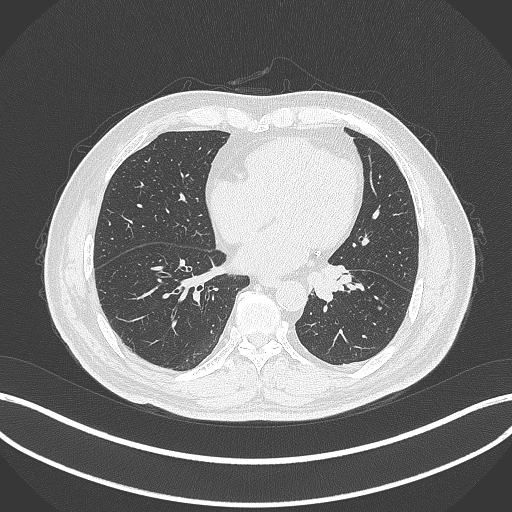
Chest CT, one axial slice; reconstruction kernel B70f; 120 kVp; lung window (W 1500 / L -600 HU); 1 mm slice thickness; 512 × 512 image matrix, field of view 400 × 400 mm. Male patient, age 71 years. From the clinical record (not read from this slice): clinical TNM (as recorded): T1b N0 M0.
Outlined on this slice (rectangle marked by the reading radiologist):
- lung tumour (recorded histology: squamous cell carcinoma): bounding box <308,263,355,304> (left, top, right, bottom; pixels)